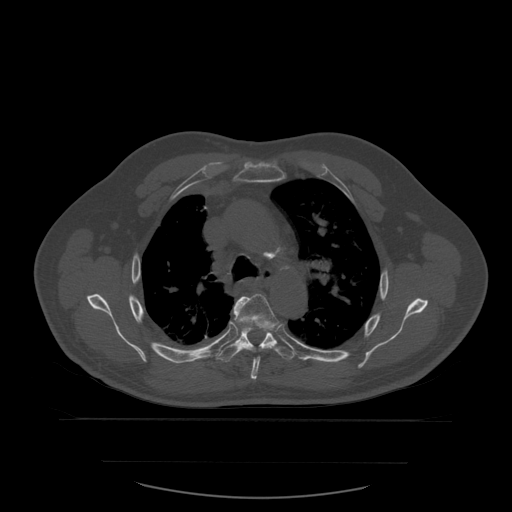
CT including the spine, one axial slice. Position 415 of 590 along the scan axis. Bone window (W 1800 / L 400 HU). 1.25 mm slice thickness. 512 × 512 image matrix. Patient age 71 years. From the clinical record (not read from this slice): primary cancer: lung.
Structures marked on this image (semi-automatically segmented with operator editing):
- T5 vertebra: box from (x=233, y=294) to (x=278, y=380) px
- T6 vertebra: (x=217, y=312)–(x=294, y=363)